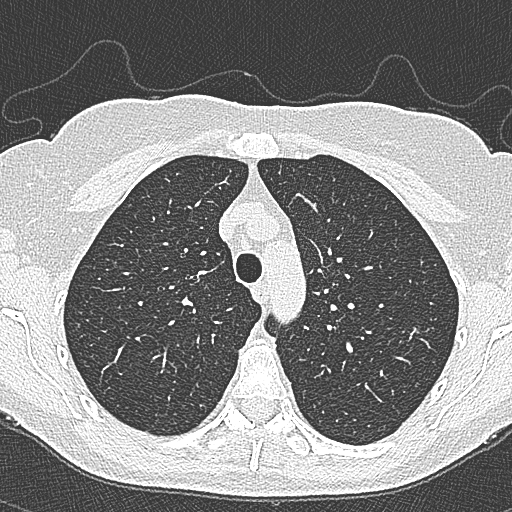
Axial slice from a low-dose chest CT screening exam; second annual screen; lung window (W 1500 / L -600 HU); slice 81 of 350 in the series; 512 × 512 image matrix. Female, age 65 years at enrolment.
• Lesion marked by an expert reader, bounding box <397,311,447,363> (left, top, right, bottom; pixels).
• The screening reader recorded 4 non-calcified nodules or masses ≥4 mm on this exam; which of them this box marks is not recorded.